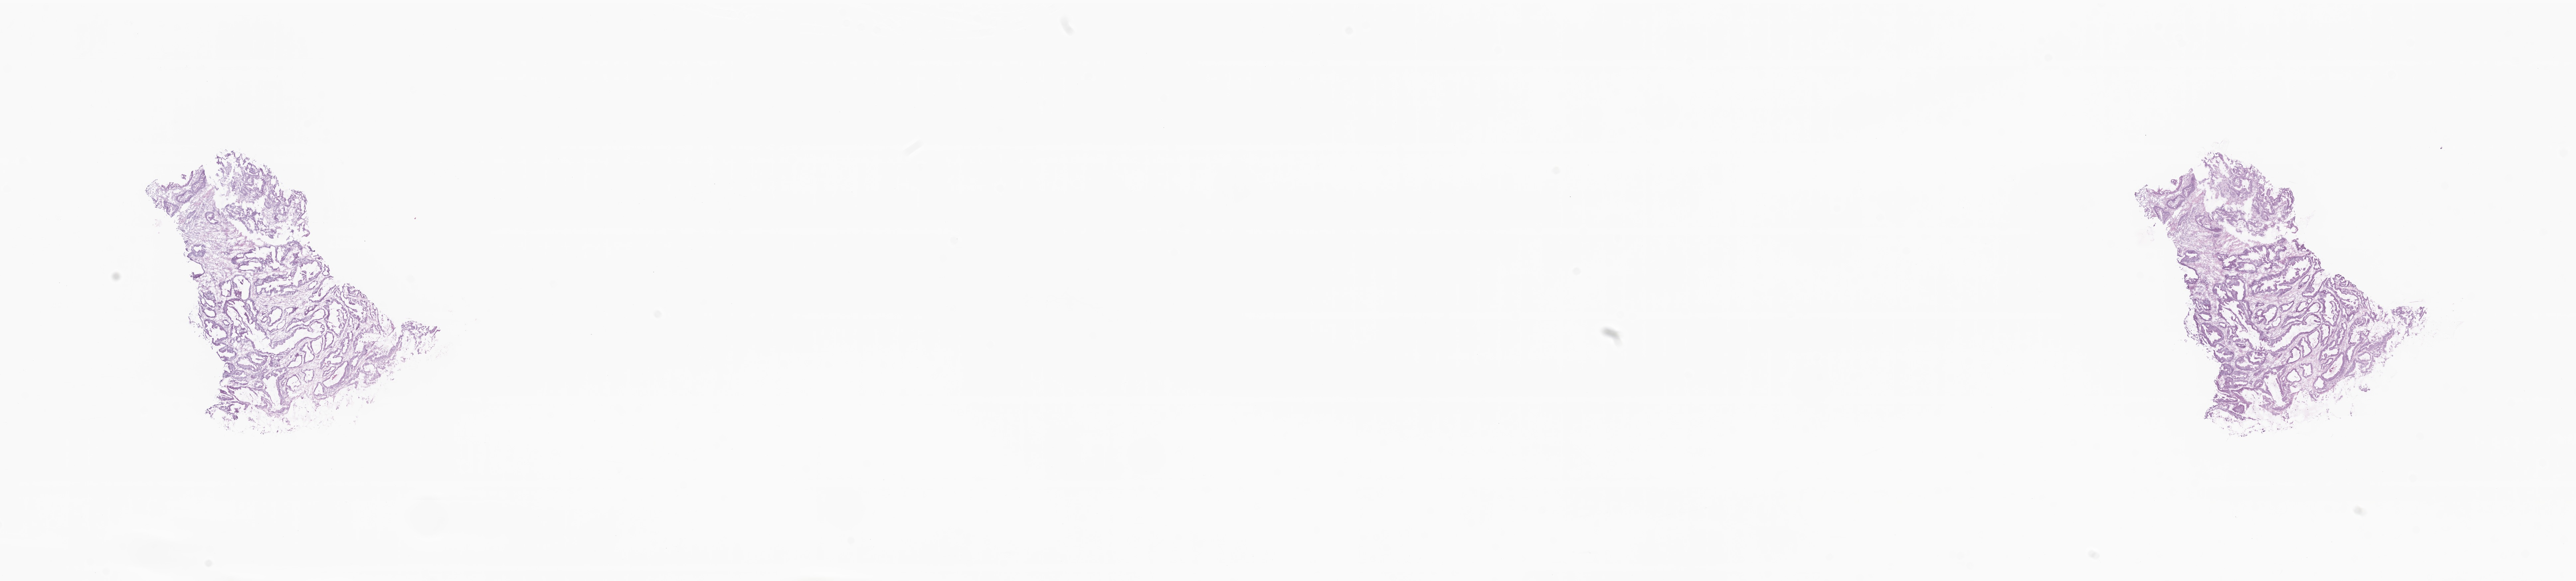
Hematoxylin and eosin (H&E) whole-slide image — whole scanned area (about 32.7 x 7.4 mm) shown as a low-resolution overview; frozen section (tissue freezing medium); primary tumor; site: ileum. Female, age 83 years at initial diagnosis. Composition of this section per pathologist review: tumor cells 30%, tumor nuclei 70%, stromal cells 65%, necrosis 1%, normal cells 4%. Infiltration values recorded for this section: lymphocyte infiltration 23%, monocyte infiltration 1%, neutrophil infiltration 0%.
- diagnosis: Adenocarcinoma, NOS